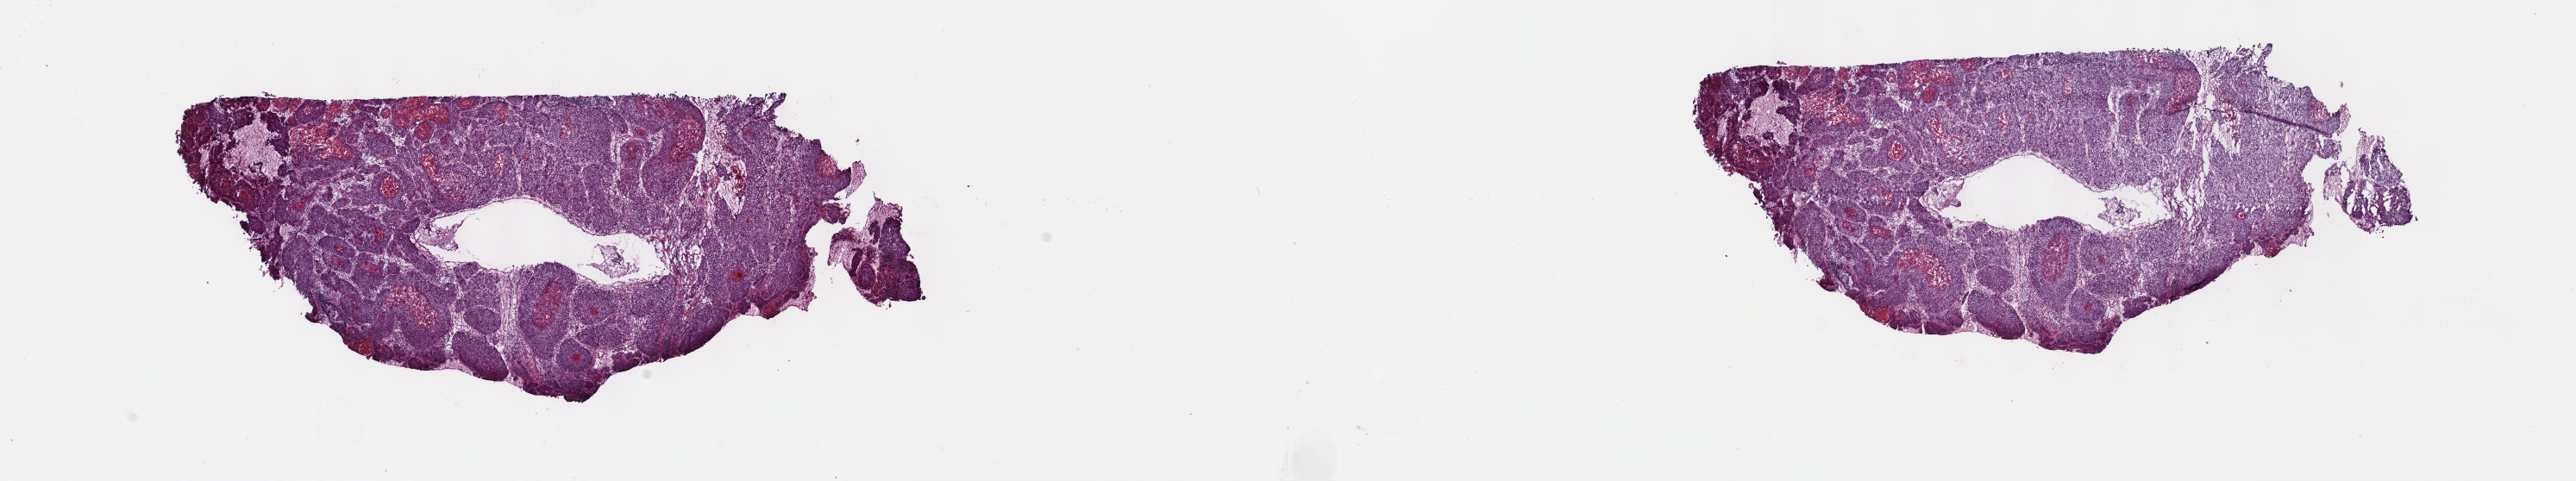
H&E-stained whole-slide image — a low-resolution overview of the entire scanned area, about 24.2 x 4.5 mm (slide scanned at 40x). Frozen section from the top of the tissue portion. Sample: primary tumour, cervix. Female, age 24 years at initial diagnosis. Histologic grade: GX (grade cannot be assessed). Pathologist review of this section (percent, as recorded): tumour cells 80%, tumour nuclei 80%, normal cells 5%, stromal cells 10%, necrosis 5%. Inflammatory infiltration, as recorded: lymphocyte infiltration 2%, monocyte infiltration 2%, neutrophil infiltration 2%.
- diagnosis: Squamous cell carcinoma, large cell, nonkeratinizing, NOS (cervix uteri)
- FIGO stage: IIB